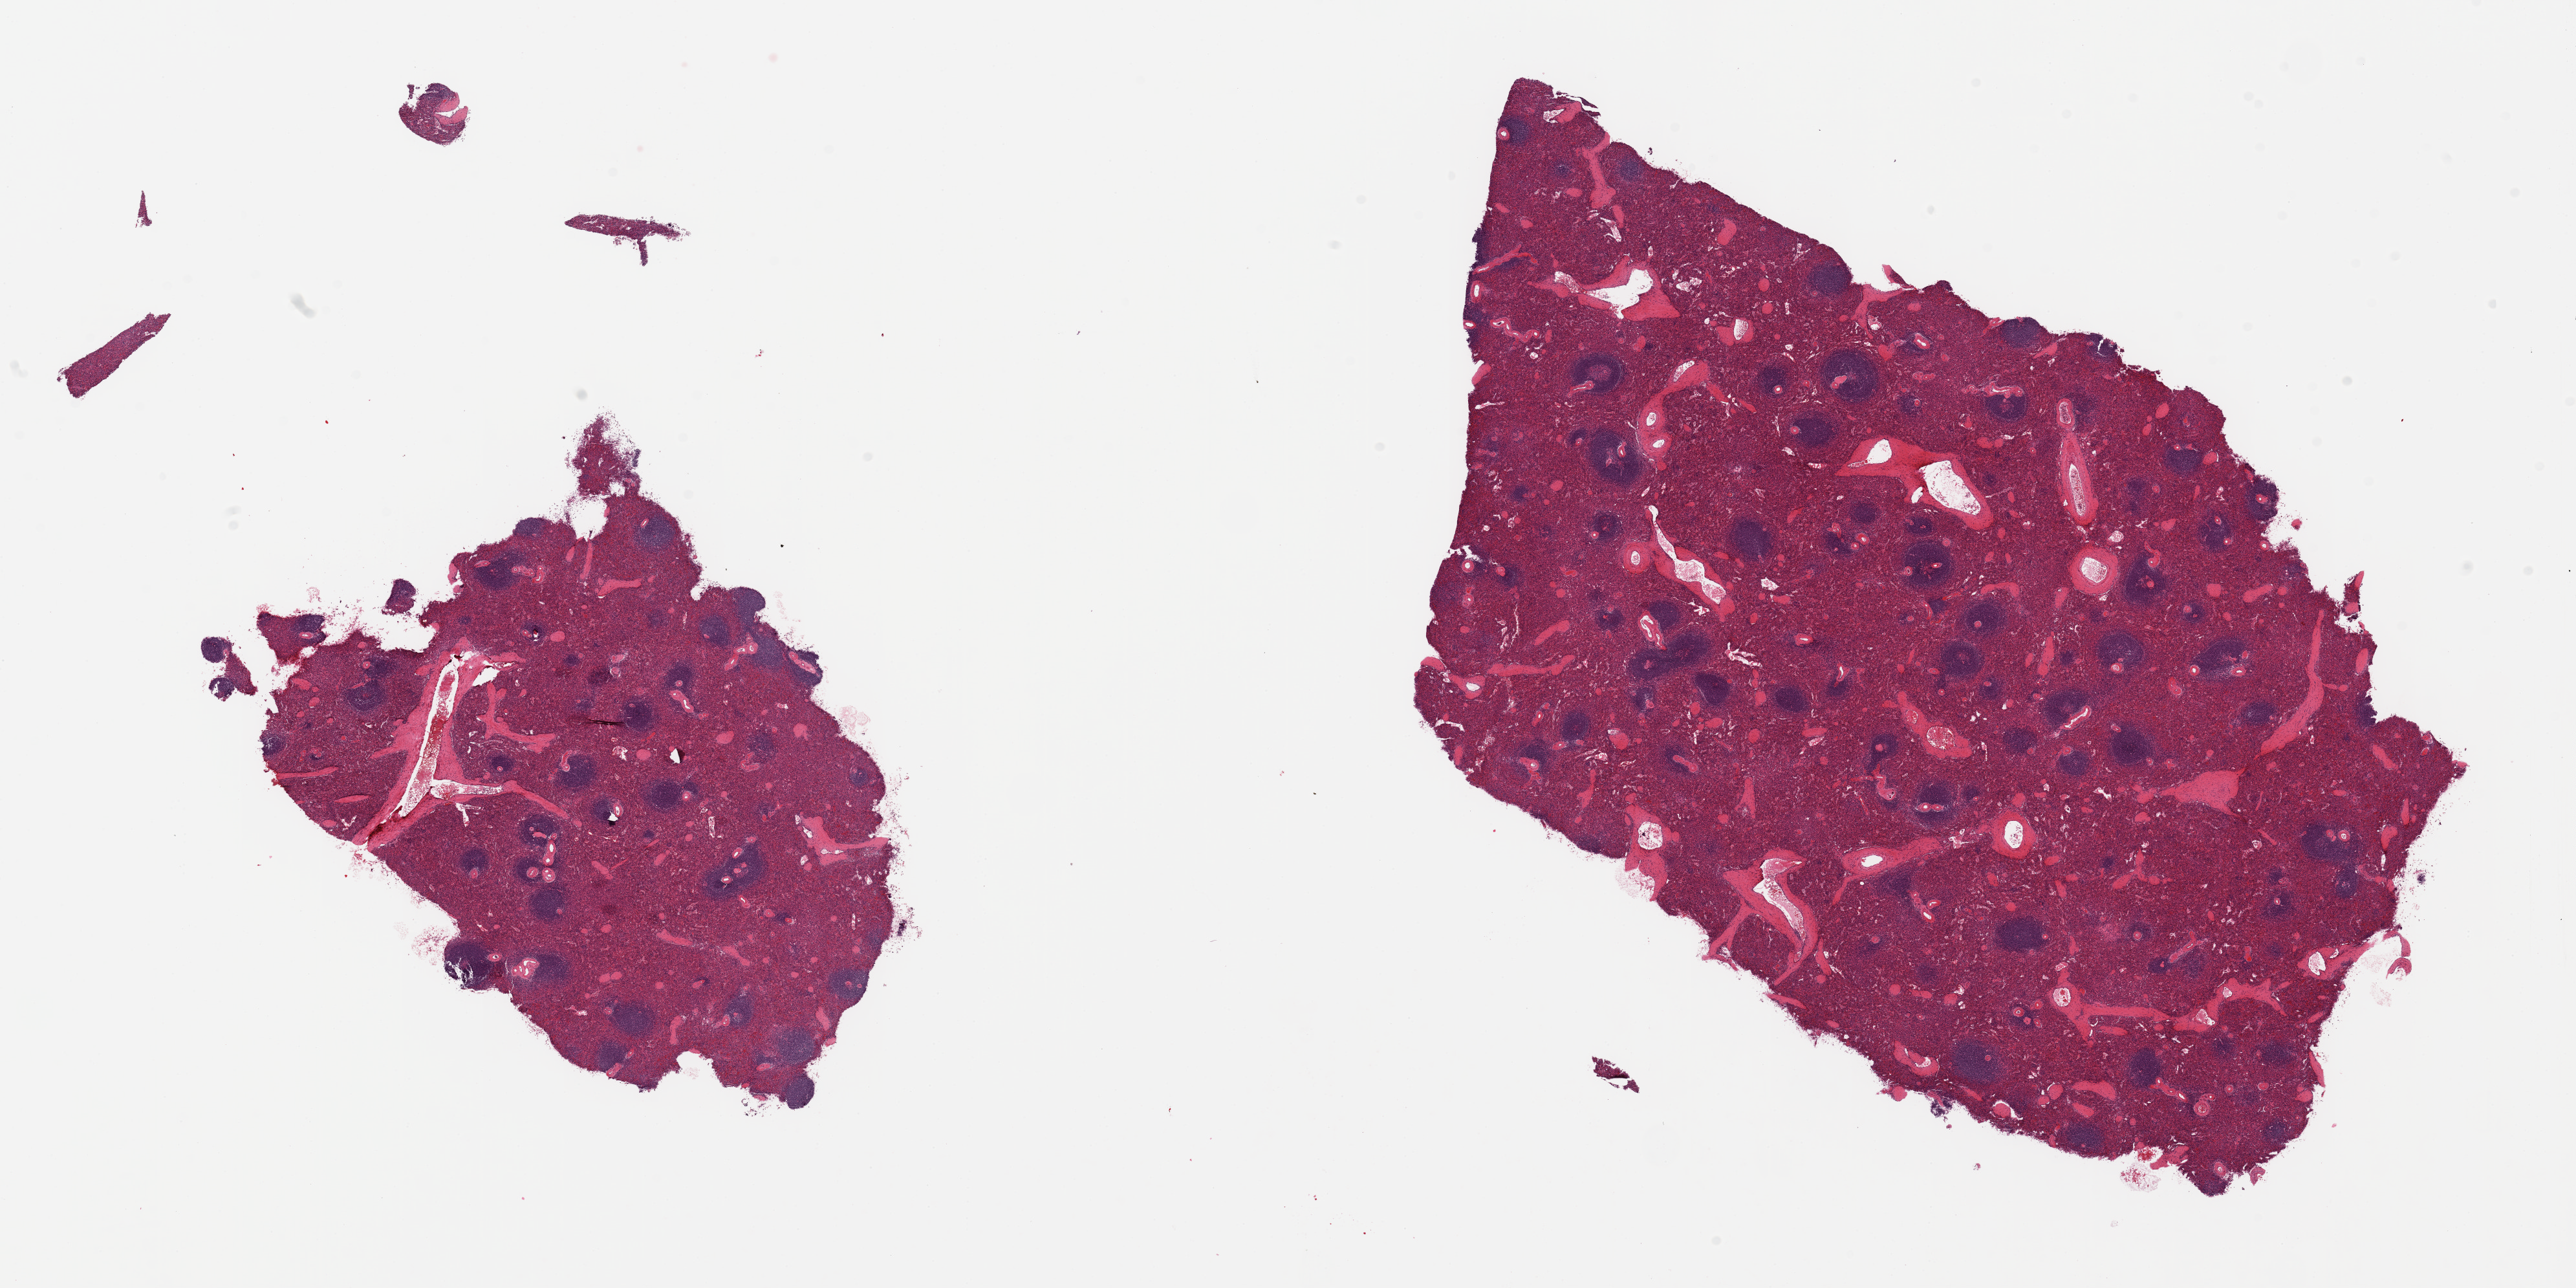
Whole-slide image, H&E stain, brightfield, low-resolution overview of the scanned area, about 31.5 x 15.7 mm. PAXgene-fixed paraffin-embedded (PFPE) section. Section of spleen (target tissue). Tissue donor sample. Female donor.
Pathologist's review note for this sample: 2 pieces, minmal congestion.